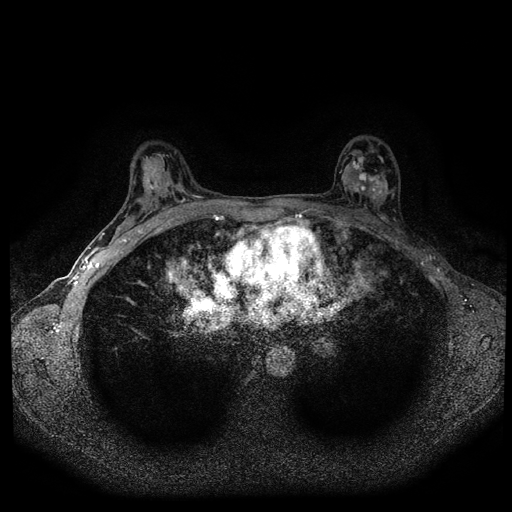
Breast MRI (dynamic contrast-enhanced, multi-phase), one axial slice; slice 57 of 108 in the series (ordered by position); dynamic contrast-enhanced series, time point 2 of 5 at this slice position (early post-contrast); 1.5 T; TE 2.7 ms, TR 5.5 ms; 2 mm slice thickness; 512 × 512 image matrix. Patient: female, 36 years.
Outlined on this slice (semi-automatic segmentation, software-assisted and operator-edited):
- breast lesion (labelled 'tumour' in the annotation; benign lesions carry a separate 'benign' label): bounding box <341,150,391,206> (left, top, right, bottom; pixels)